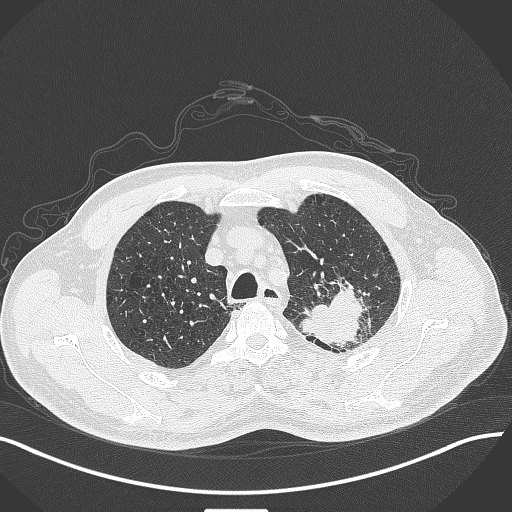
Chest CT, one axial slice. Slice 337 of 429 in the series (ordered by position). 120 kVp. Lung window (W 1500 / L -600 HU). 1 mm slice thickness. 512 × 512 image matrix, field of view 400 × 400 mm. Patient: male, 55 years. Case-level facts recorded for this patient, not image findings: clinical TNM (as recorded): T3 N0 M1c; histopathological grade: G3.
Structures marked on this image (bounding box drawn by a radiologist):
- lung tumour (recorded histology: adenocarcinoma): bounding box [x1, y1, x2, y2] px = [295, 278, 371, 350]